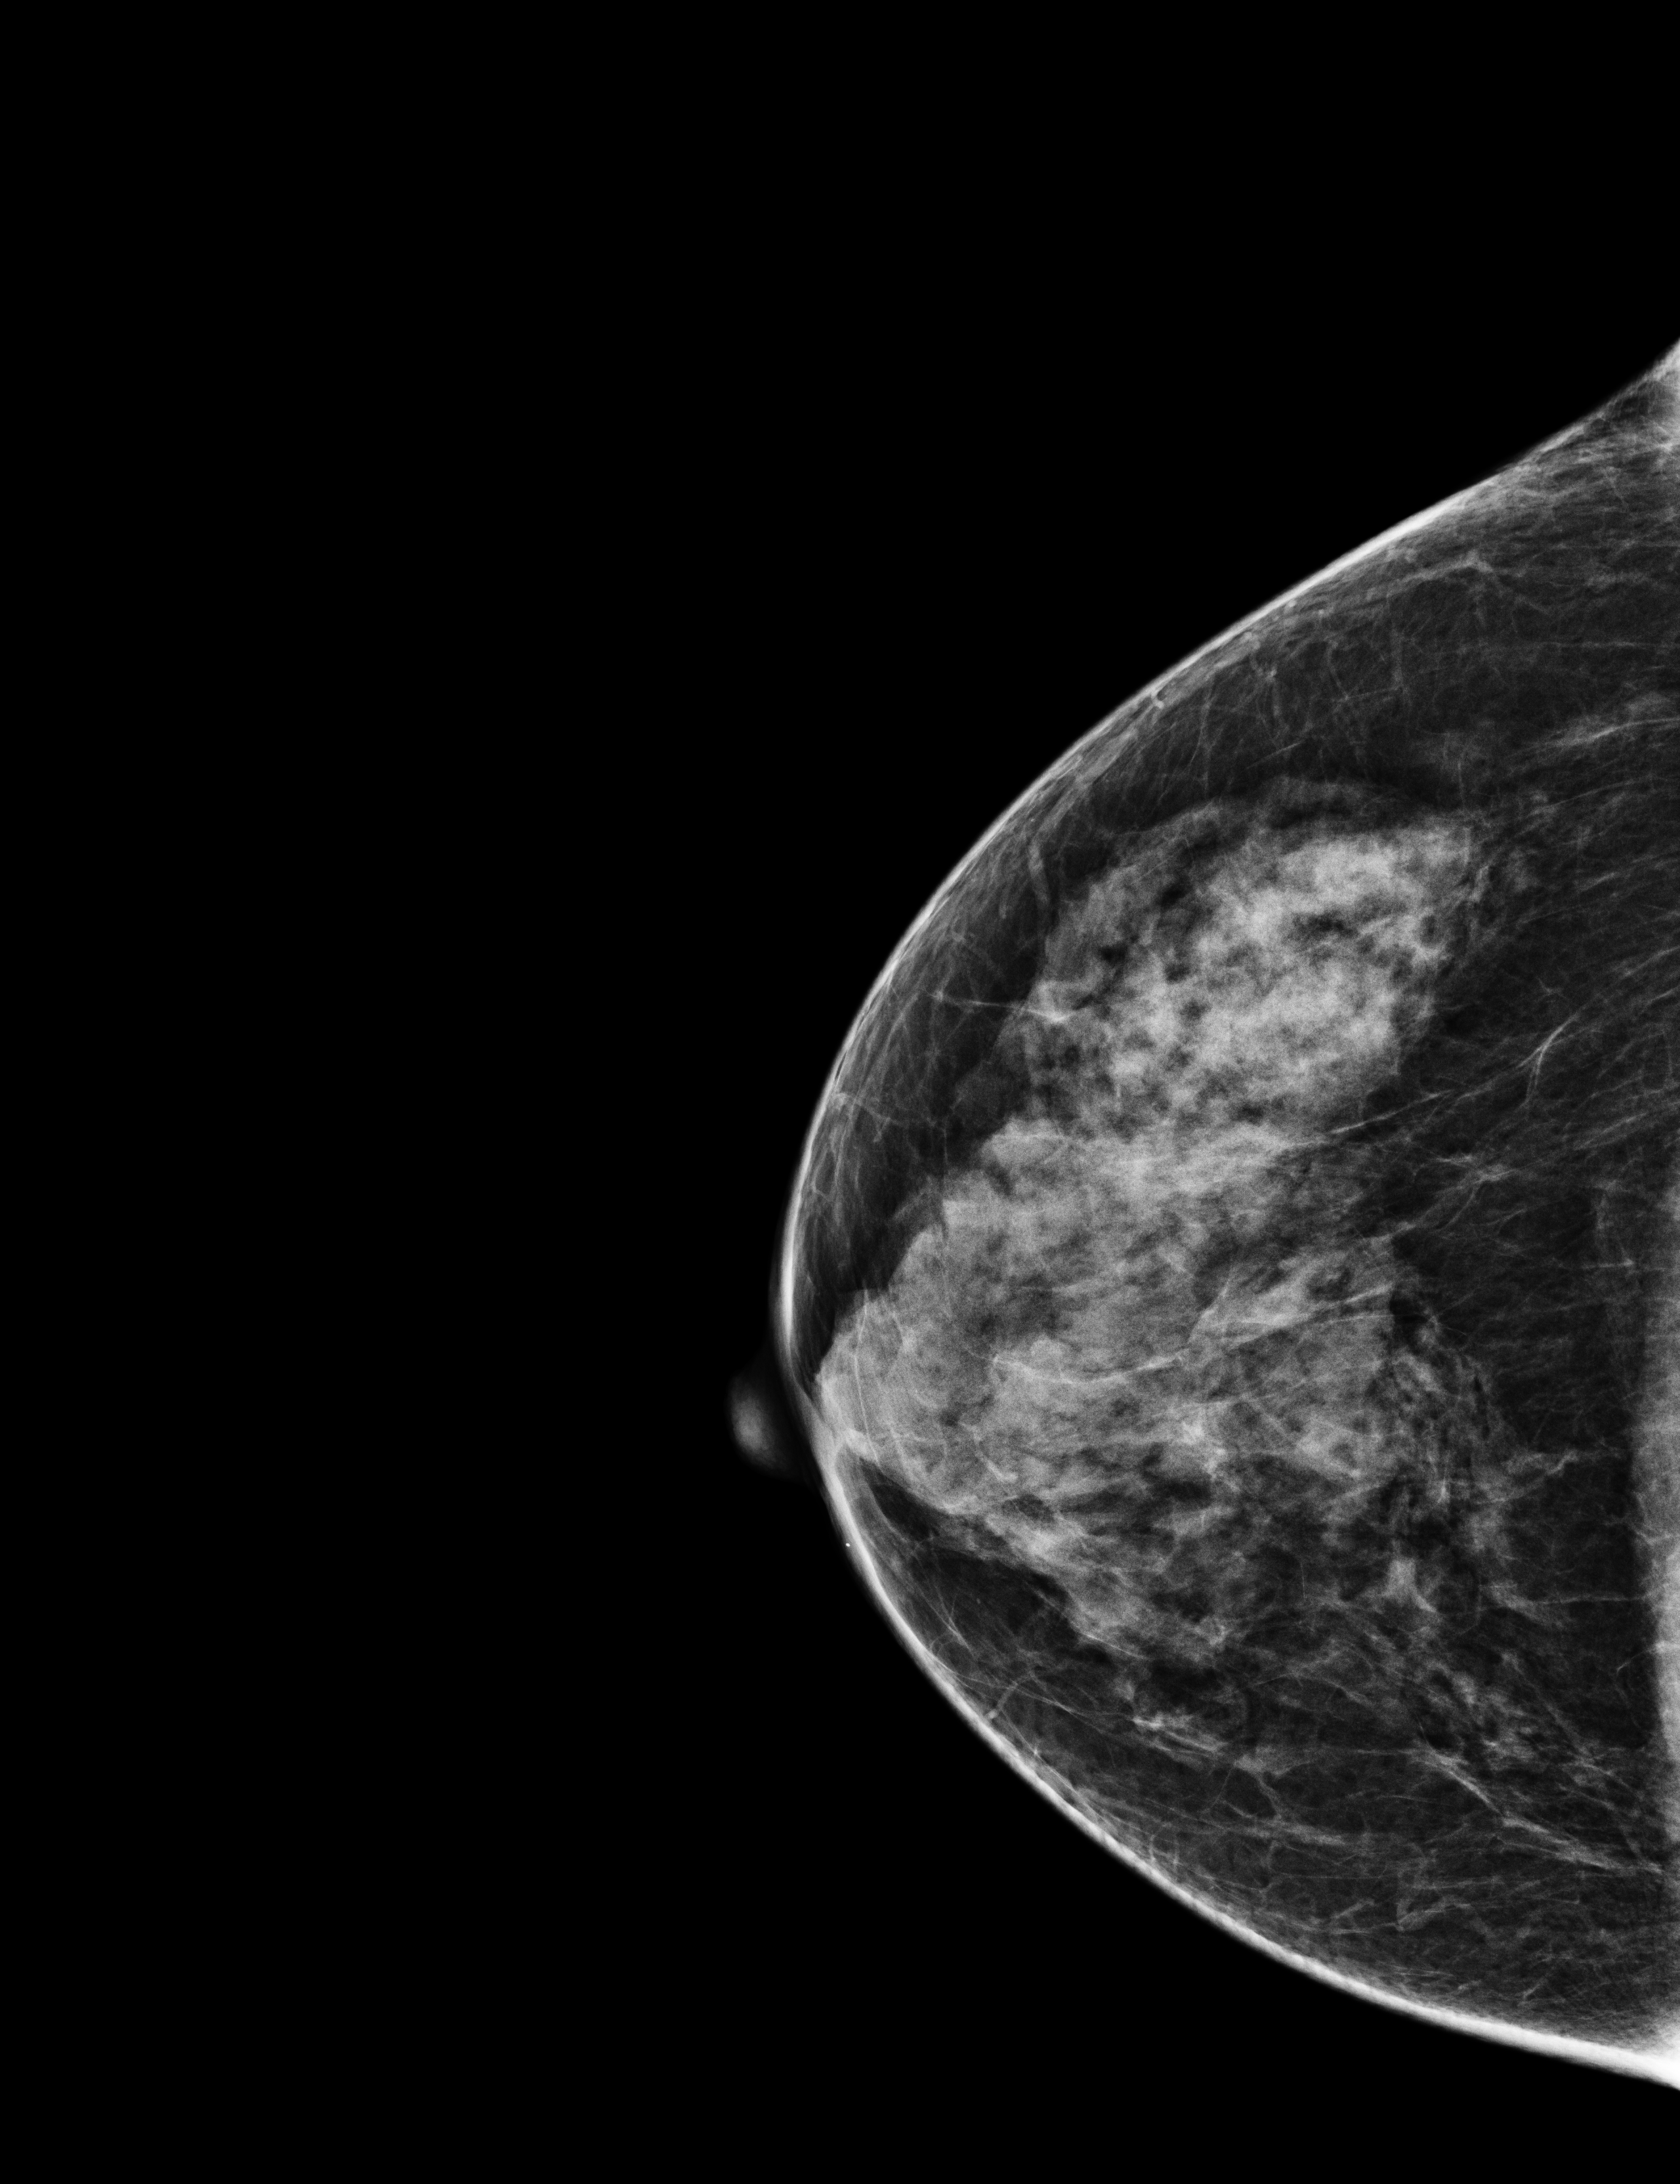
Annual screening mammography examination. Female patient, age 67 years.
Image type: full-field digital mammogram. Breast: right. Projection: cranio-caudal projection.